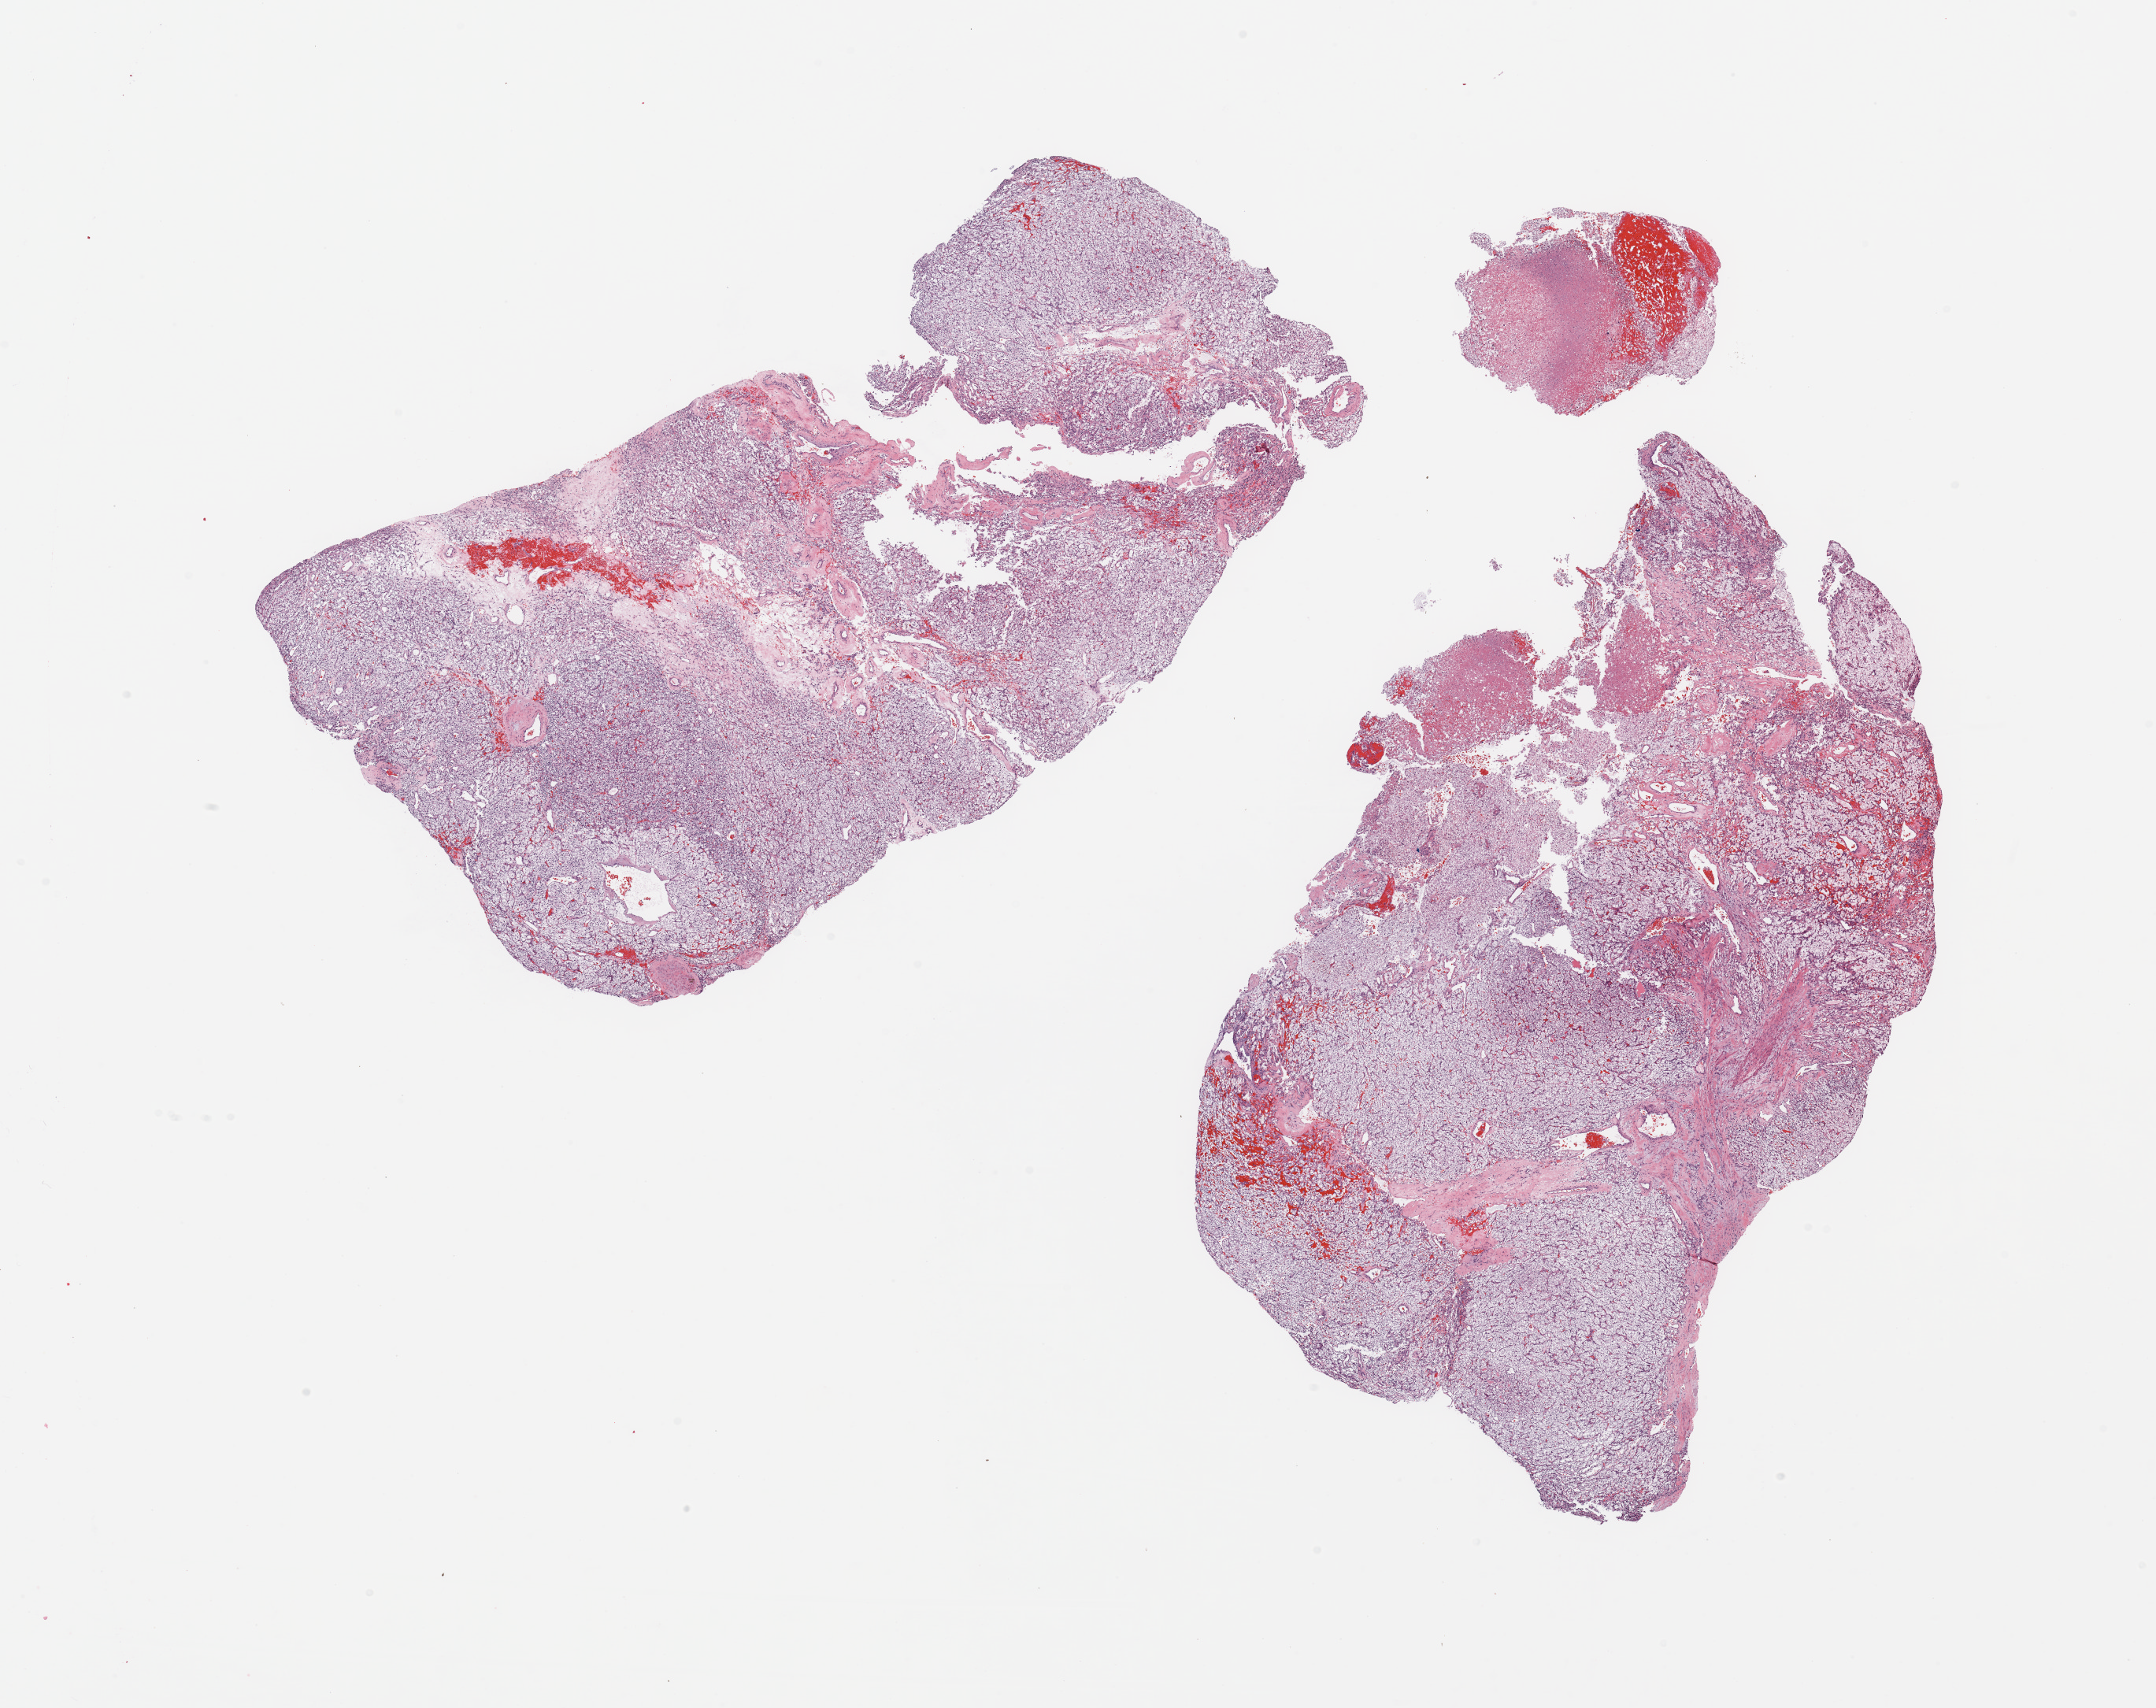
Digitized Hematoxylin and eosin (H&E) stained tissue section (whole slide) — shown as a low-resolution overview of the whole scanned area (about 21.7 x 17.2 mm, from a 20x scan). Tumour tissue sample, kidney. Patient: male, age 76 years. Histologic grade: G3 (poorly differentiated).
Diagnosis: Renal cell carcinoma, NOS. AJCC pathologic stage: III.